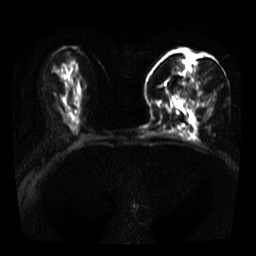
Breast MRI, one axial slice. Slice 16 of 39 in the series (ordered by position). Diffusion-weighted series; image 2 of 4 stored at this slice position (different b-values; order by instance number). 3 T. 5 mm slice thickness. 256 × 256 image matrix, field of view 320 × 320 mm. Female patient.
Structures marked on this image (expert manual segmentation):
- tumour on diffusion-weighted imaging: bounding box (x1, y1, x2, y2) in pixels: (167, 92, 173, 100)